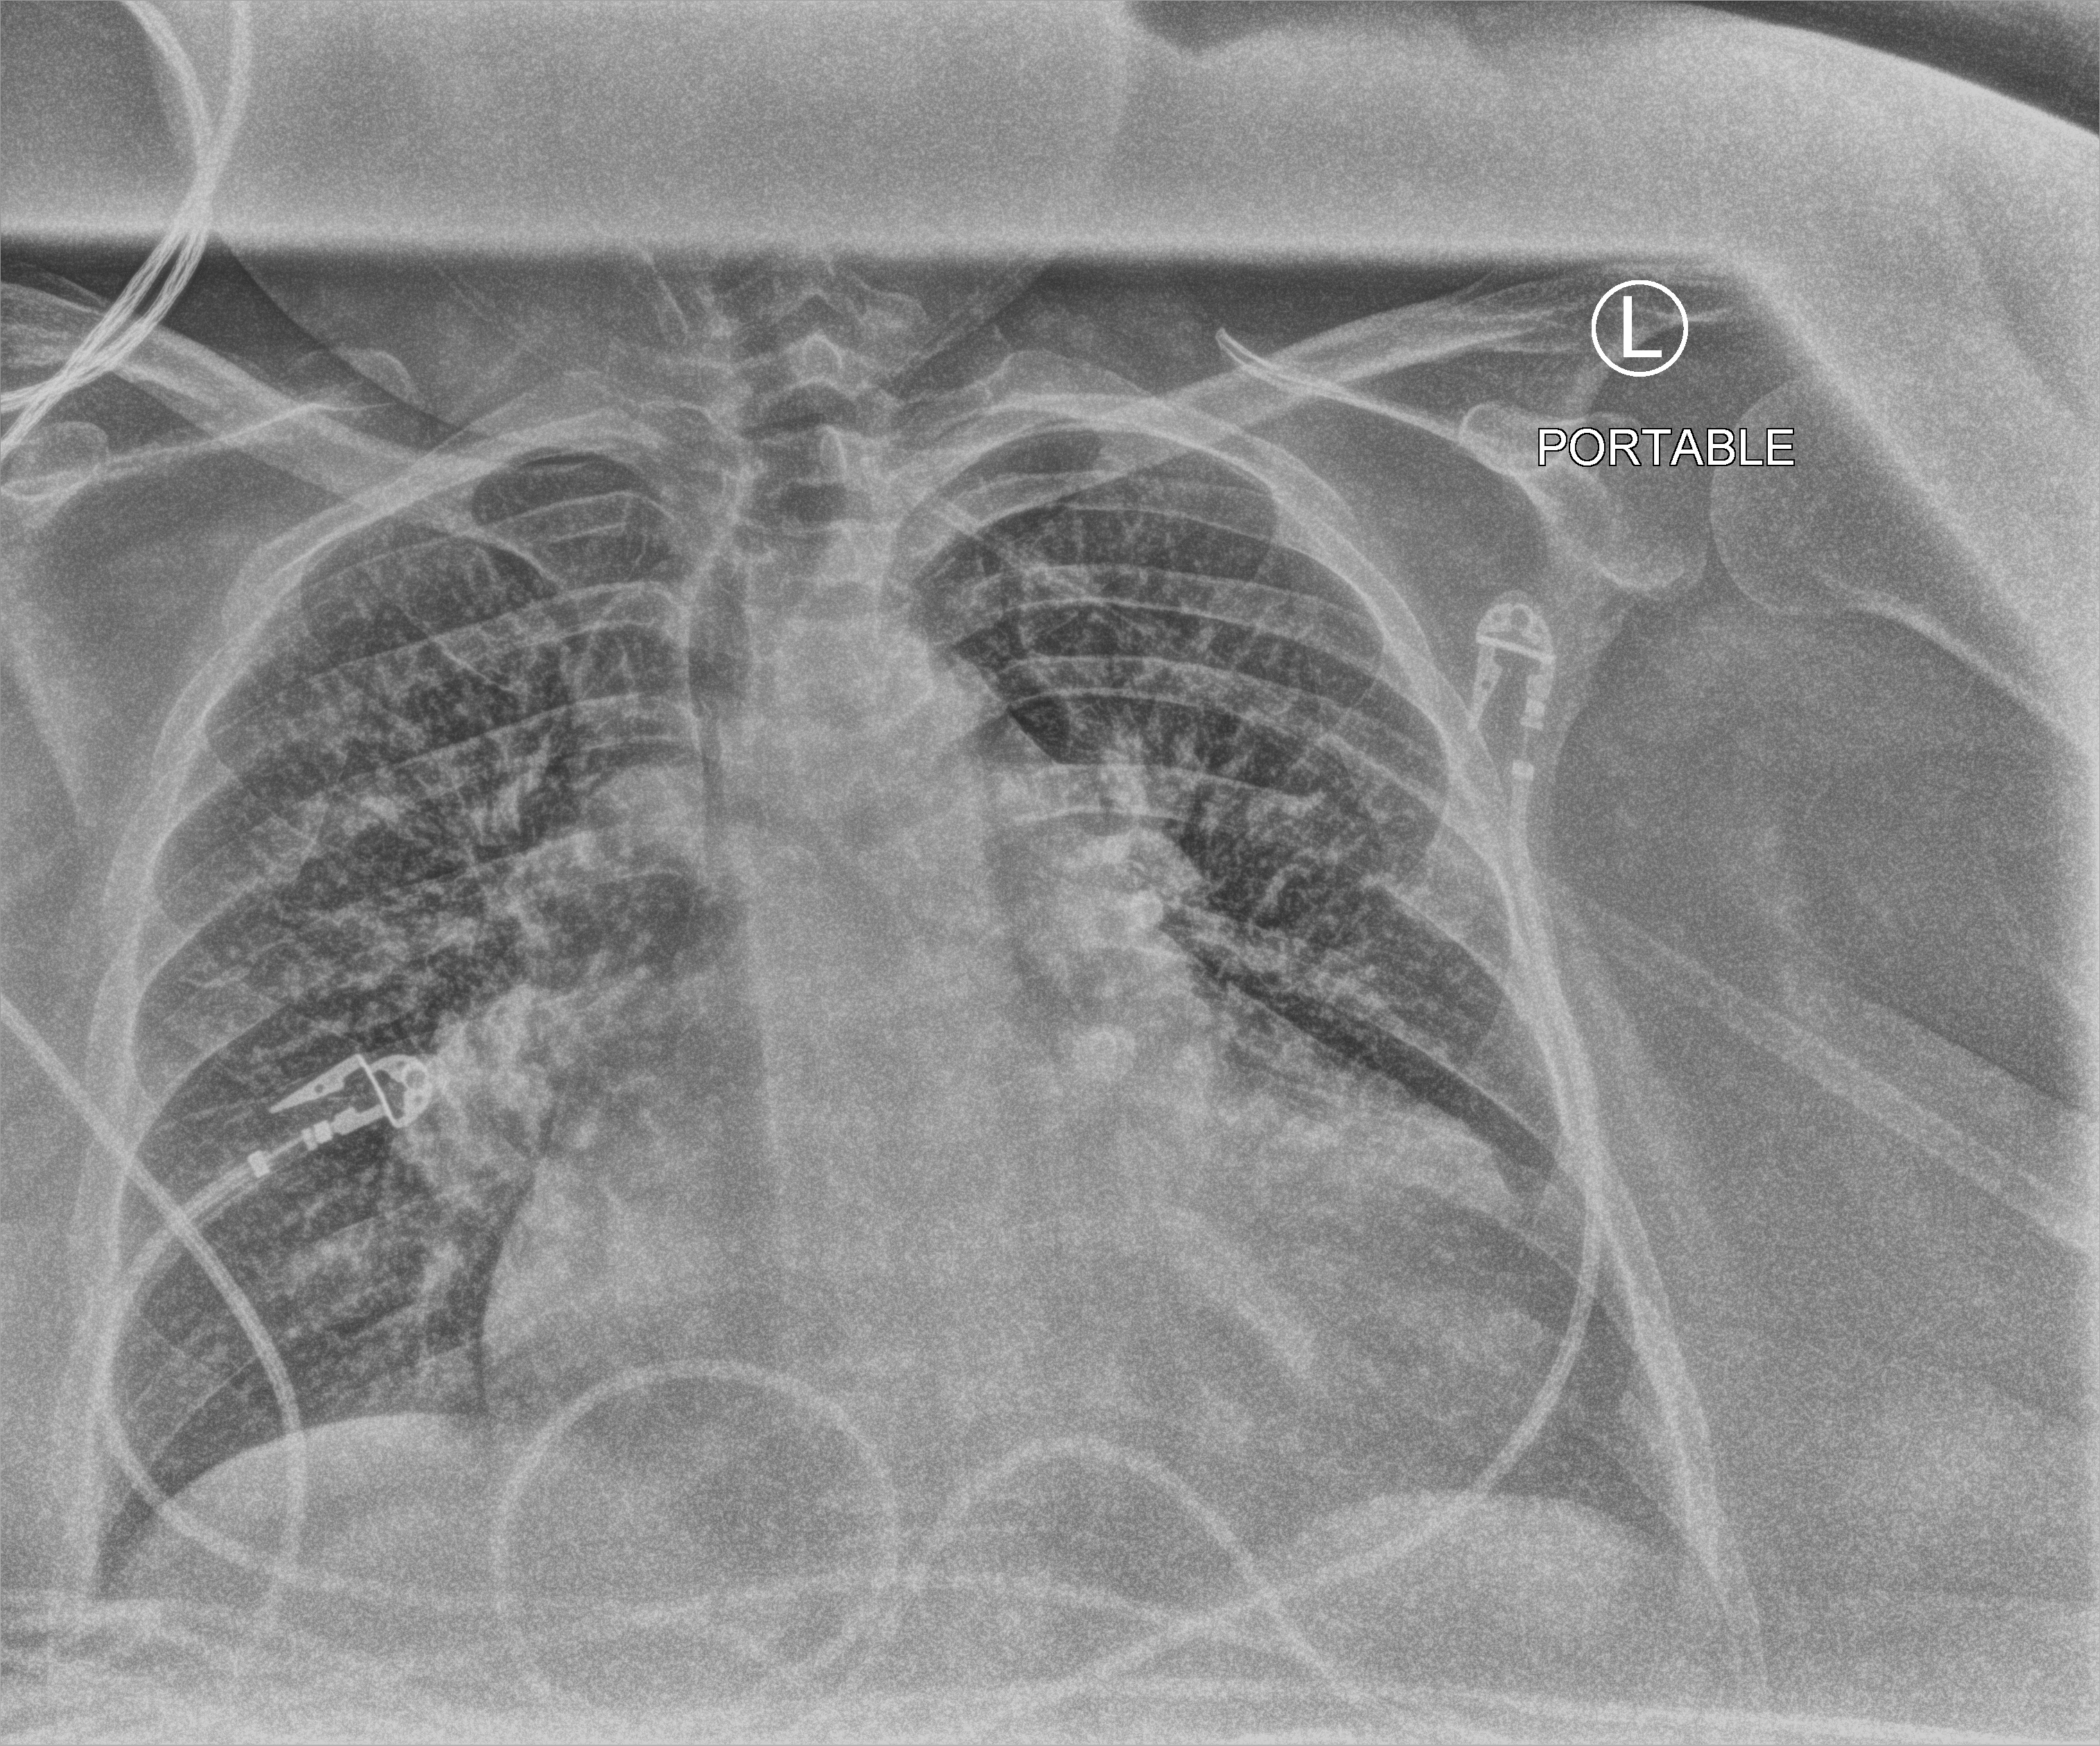
Portable chest radiograph; anteroposterior (AP) projection. Female patient hospitalised with COVID-19, age 60–74 years.
From the hospital-stay record, not from the radiograph (when in the stay this image was taken is not recorded): mechanically ventilated during this hospital stay: yes.